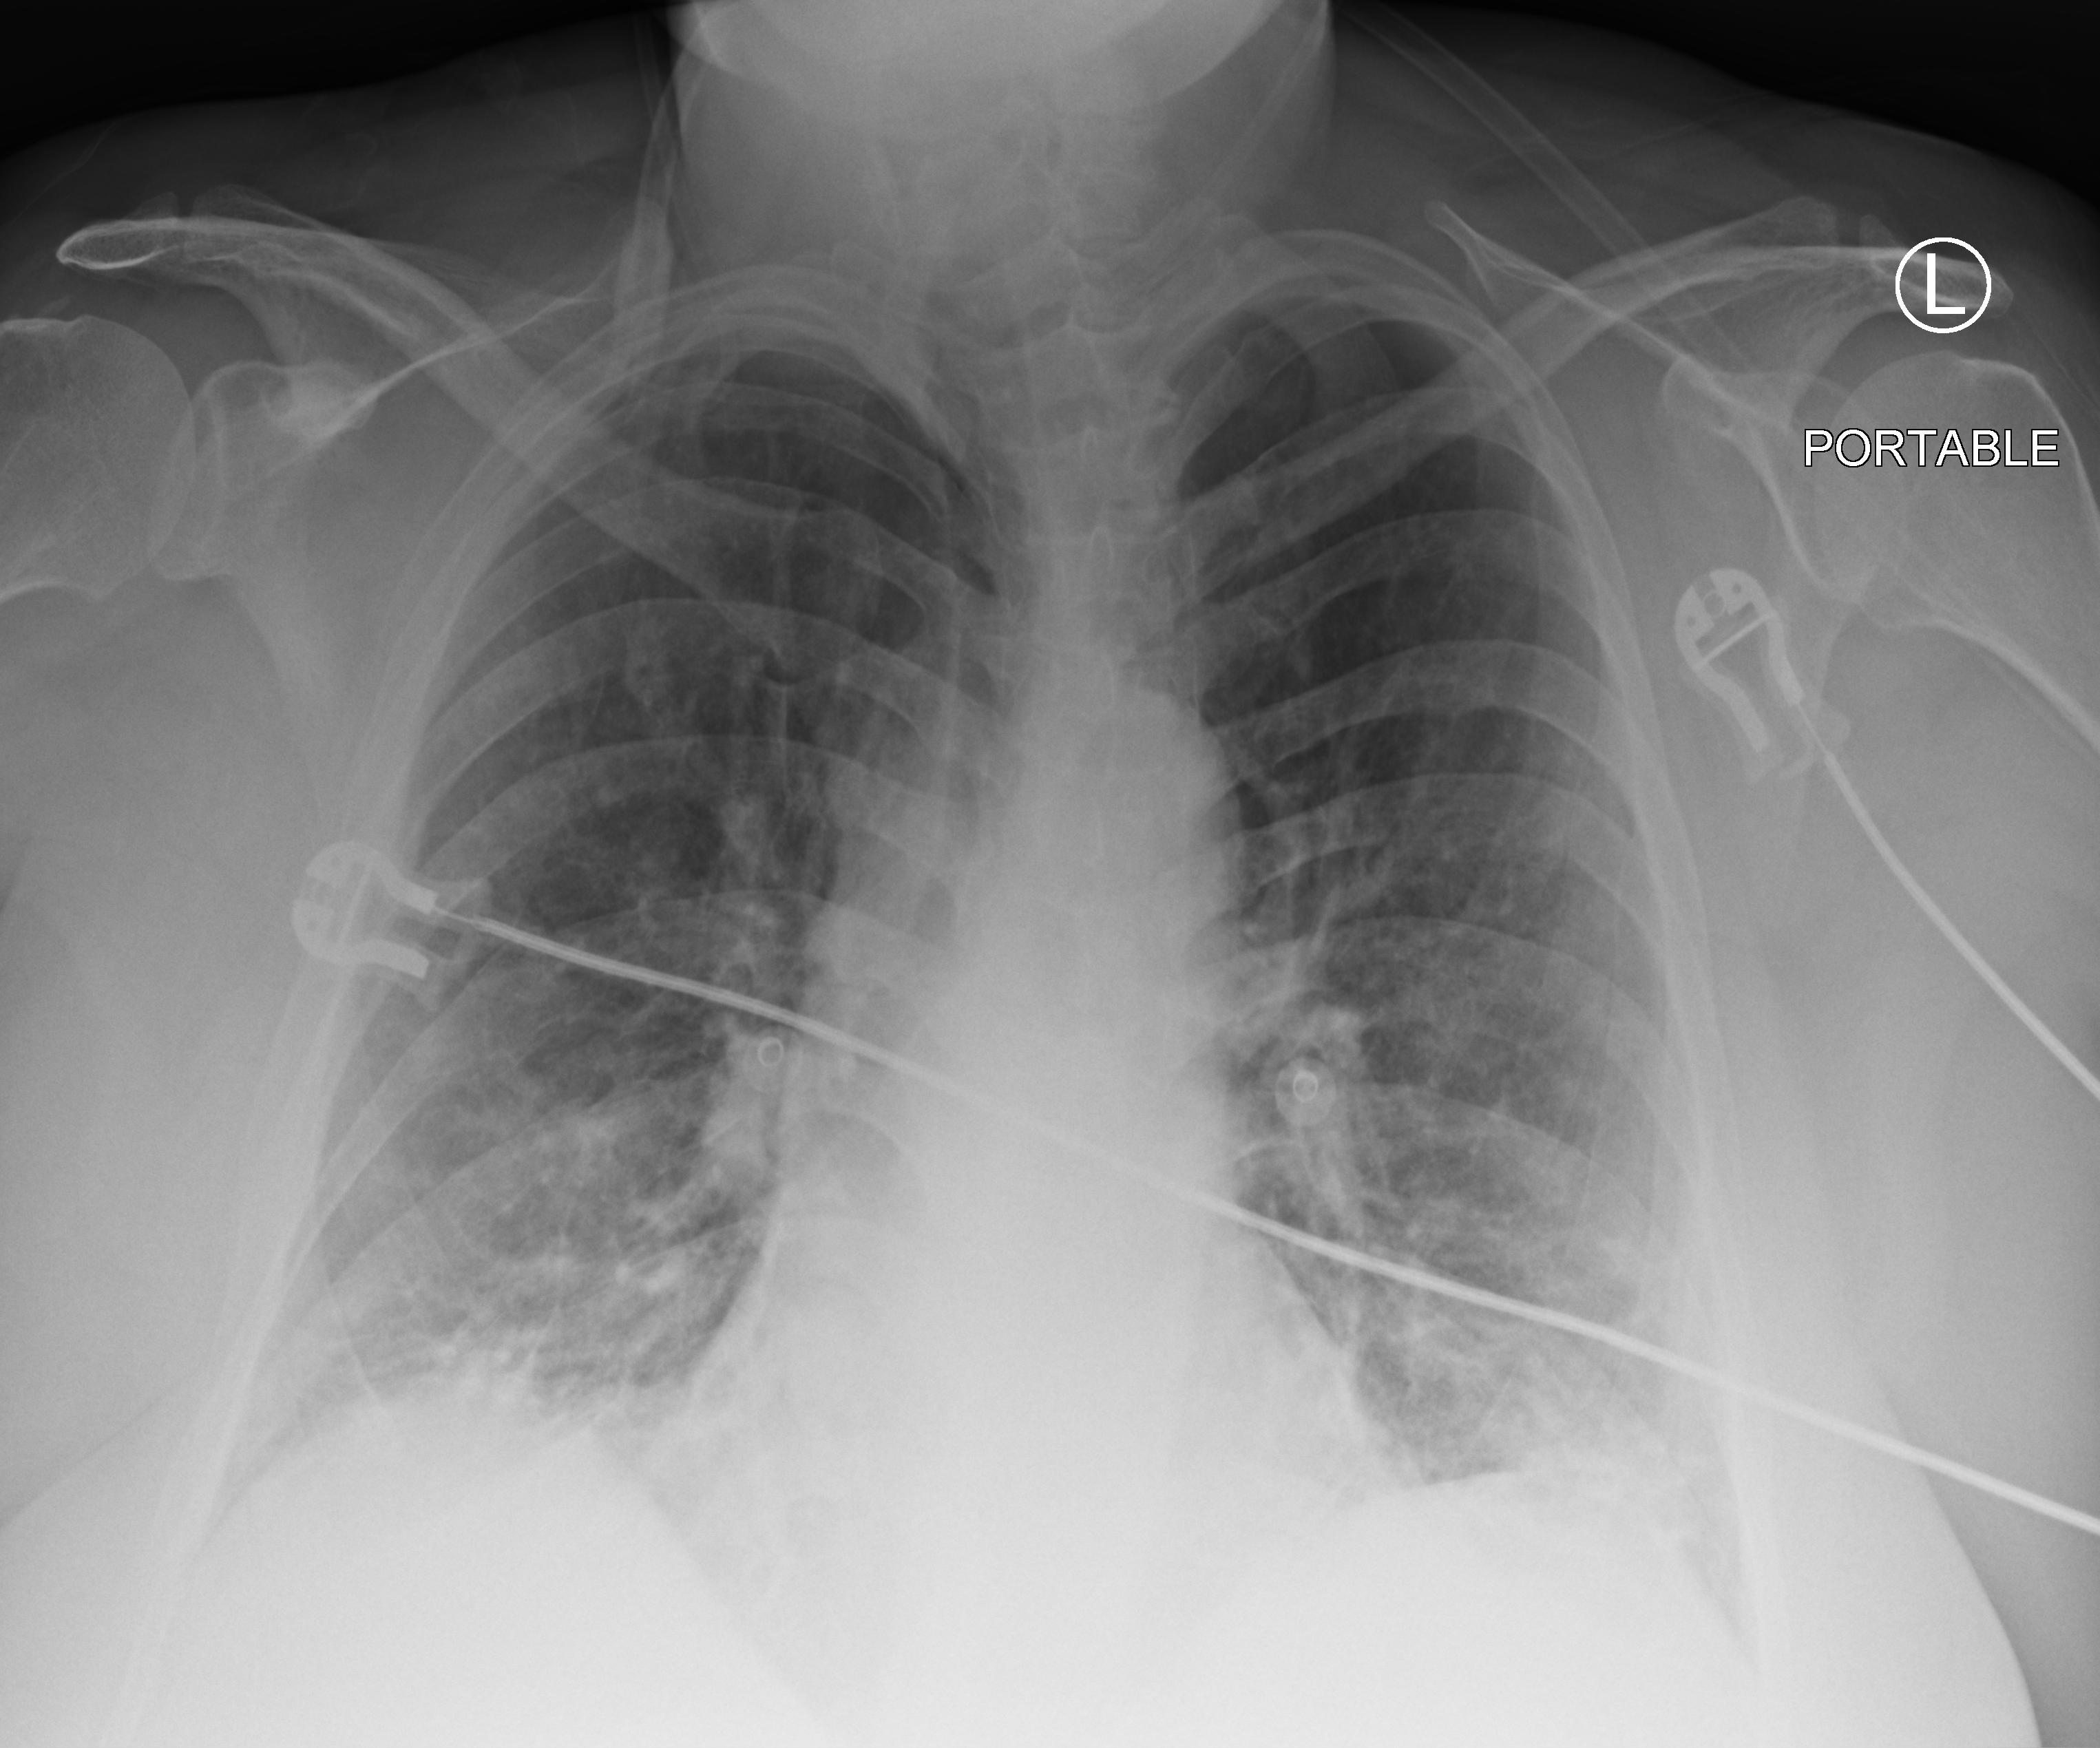
Portable chest radiograph; anteroposterior (AP) projection. Female patient hospitalised with COVID-19, age 18–59 years.
Hospital-stay facts (about this admission, not read from this image; timing relative to this image not recorded): chronic kidney disease (admission record): no; admitted to intensive care during this hospital stay: no; mechanically ventilated during this hospital stay: no.